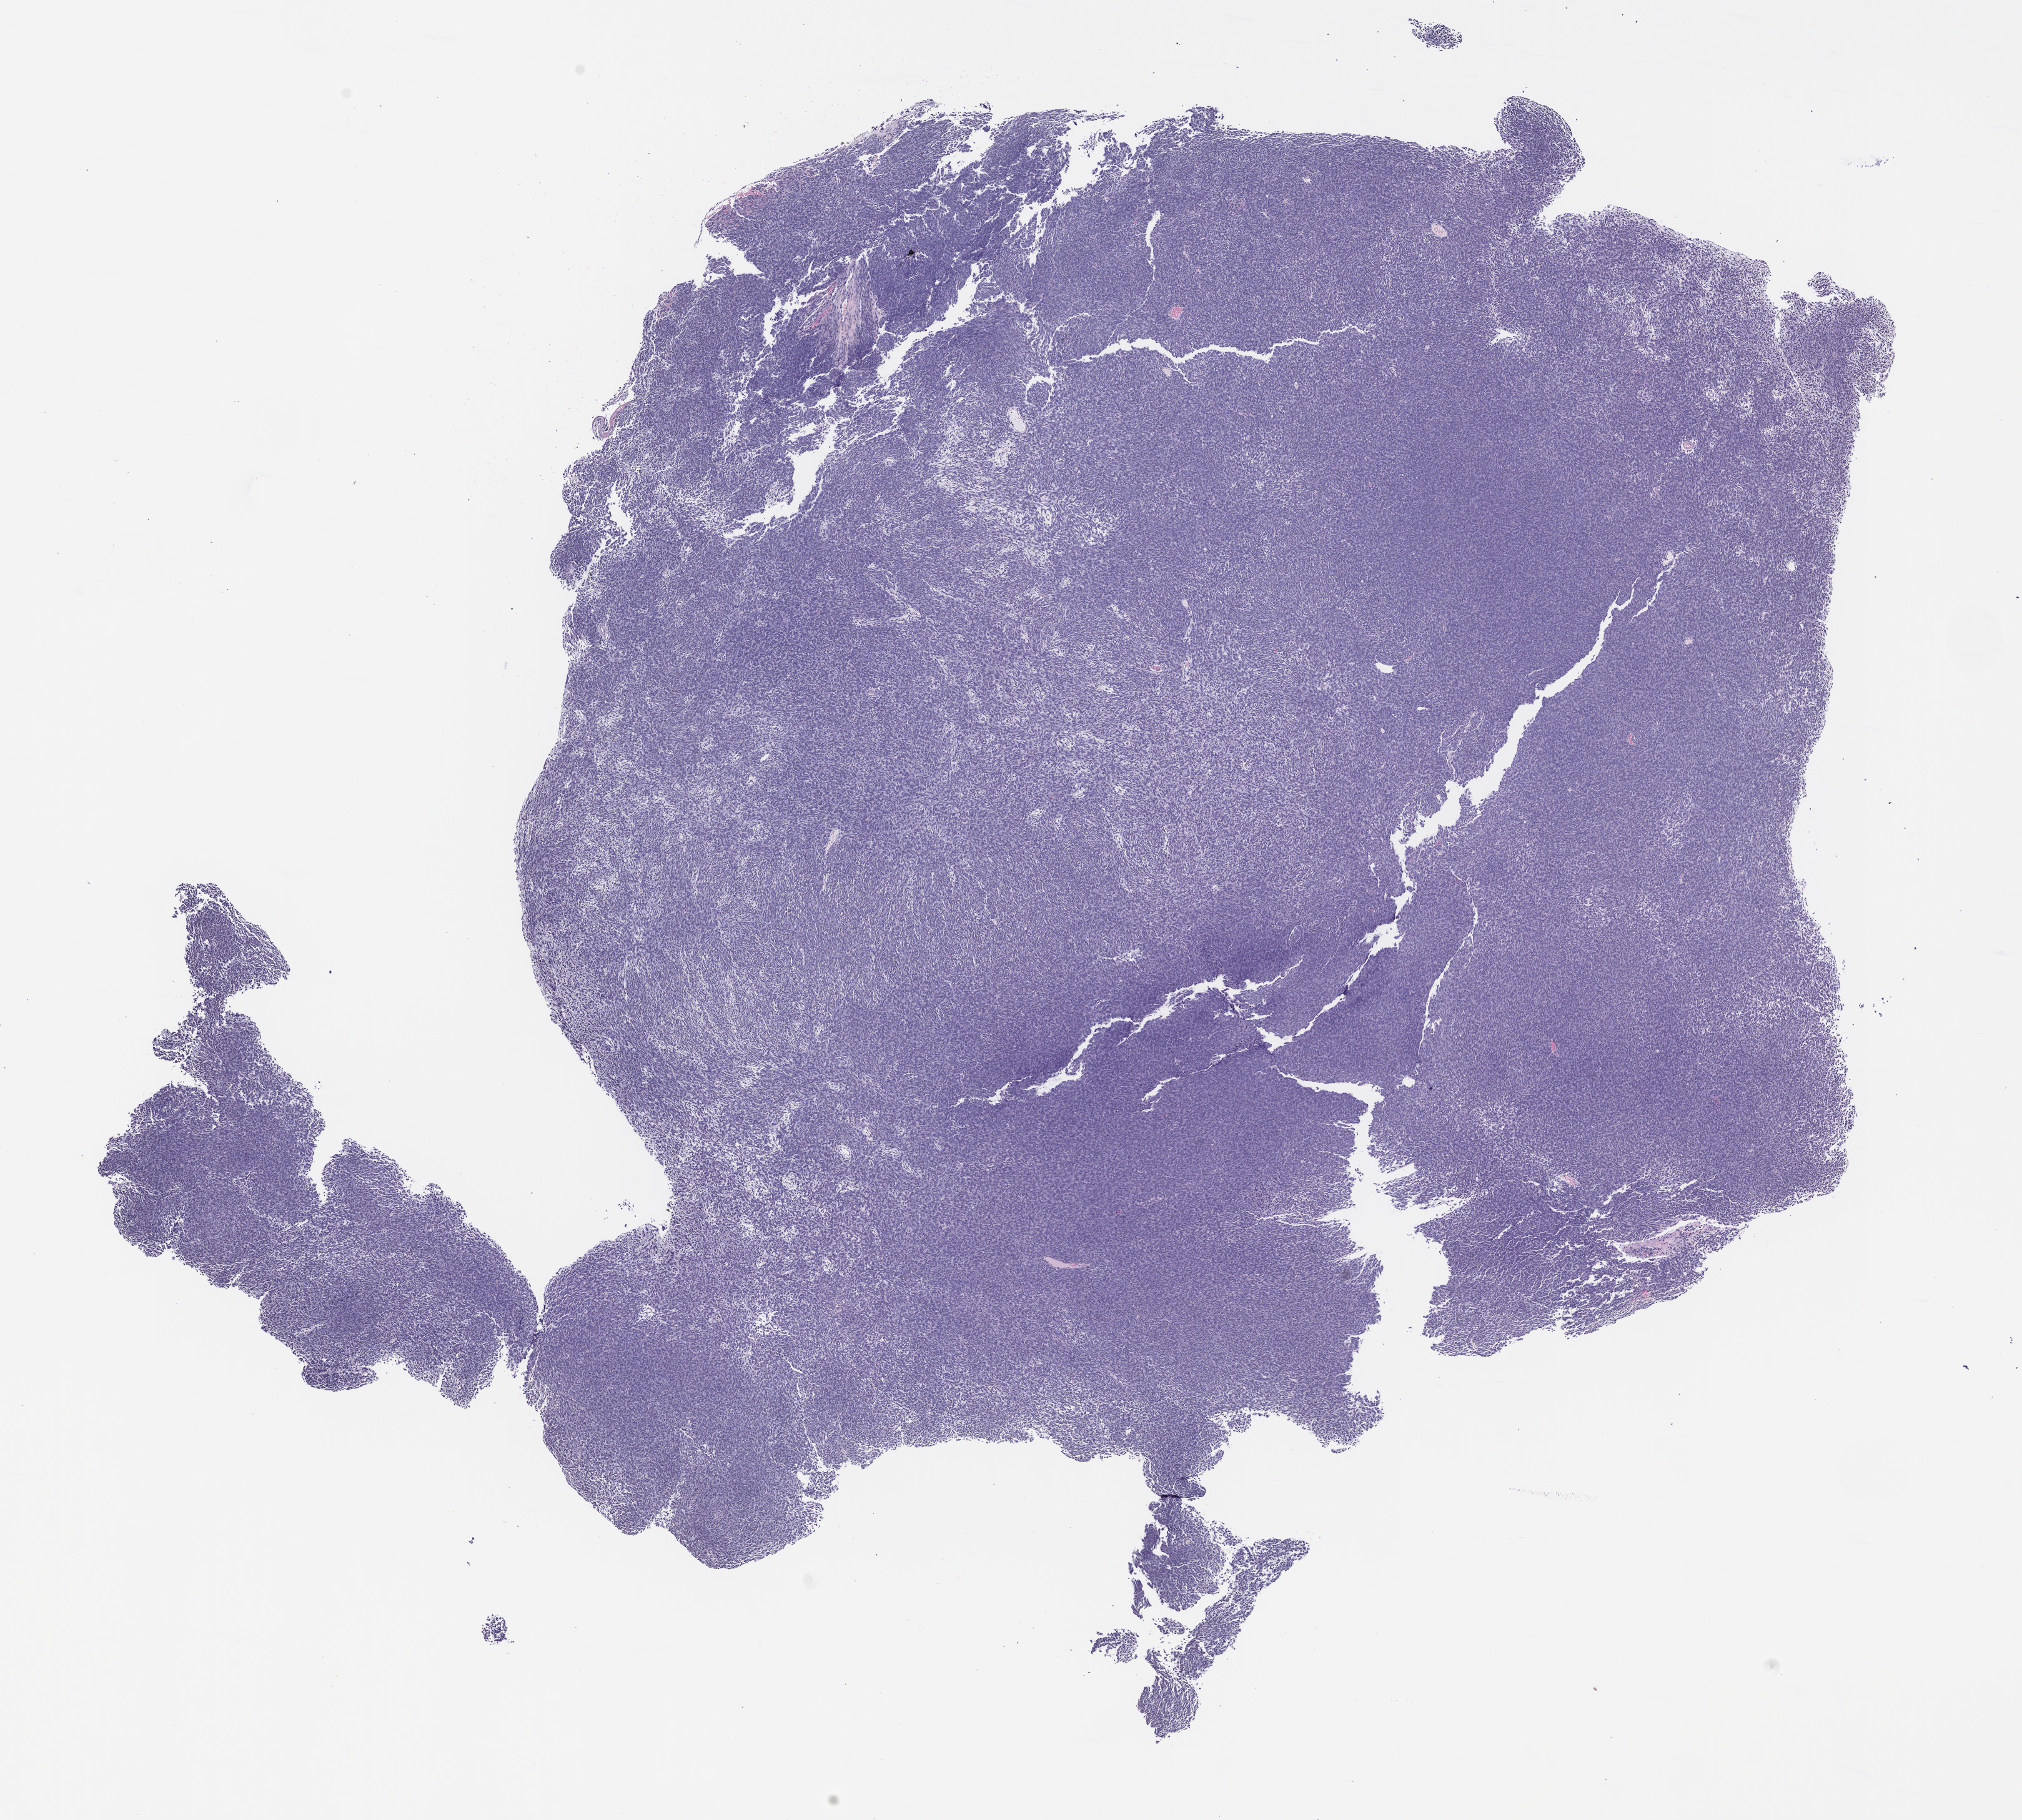
Whole-slide image, hematoxylin and eosin (H&E): patient-derived xenograft (human tumor grown in a mouse), passage 2 — a low-resolution overview of the entire scanned area, about 13.0 x 11.7 mm, FFPE section, originating tumor site category: musculoskeletal.
Originating patient diagnosis: Synovial Sarcoma.